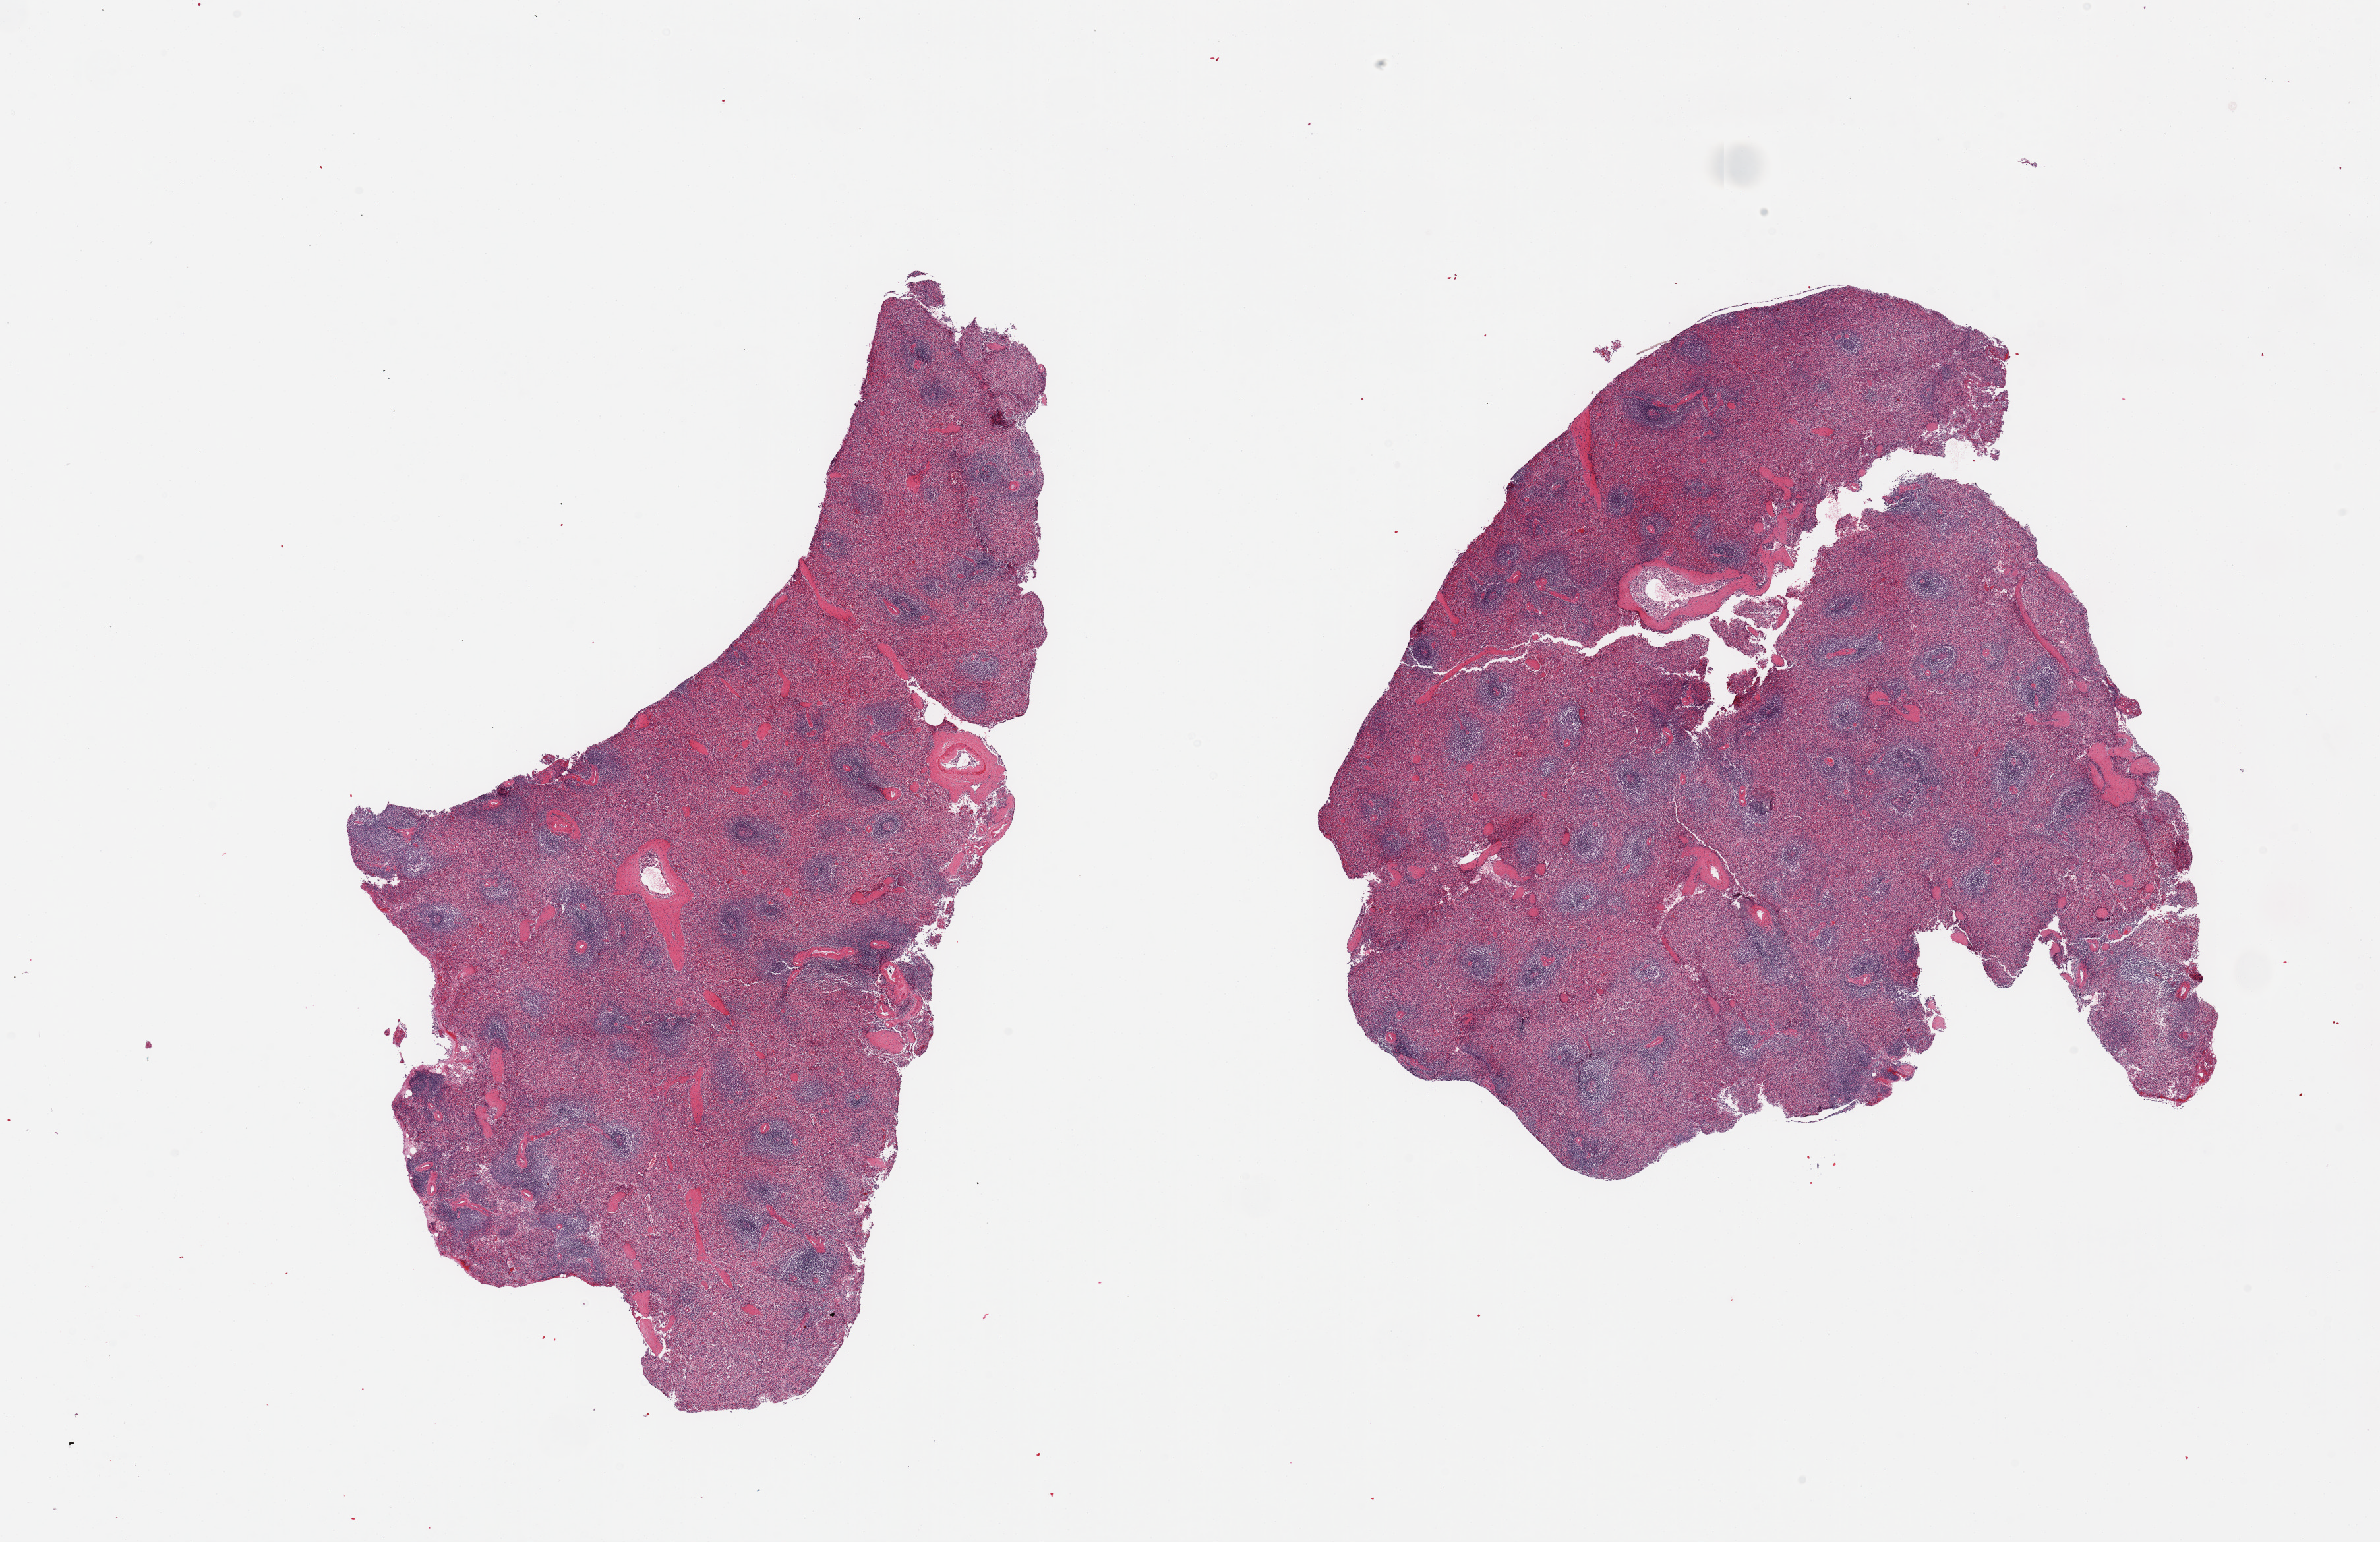
H&E whole-slide image, a low-resolution overview of the entire scanned area, about 28.5 x 18.5 mm; PAXgene-fixed, paraffin-embedded tissue; target tissue: spleen; donor tissue sample. Donor: male.
Reviewer comment on this tissue sample: 2 pieces.